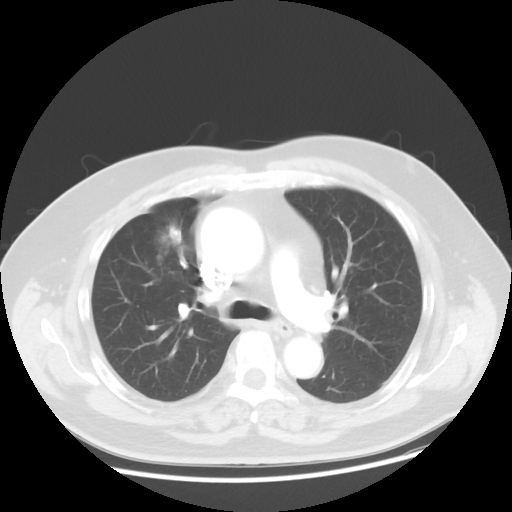
Chest CT, one axial slice. Slice 30 of 48 in the series (ordered by position). Reconstruction kernel STANDARD. 120 kVp. Lung window (W 1500 / L -600 HU). 5 mm slice thickness. 512 × 512 image matrix. Male patient, age 60 years. From the clinical record (not read from this slice): clinical TNM (as recorded): T2 N3 M0; histopathological grade: G2-3.
Structures marked on this image (rectangle marked by the reading radiologist):
- lung tumour (recorded histology: adenocarcinoma): bounding box [x1, y1, x2, y2] px = [151, 219, 191, 256]